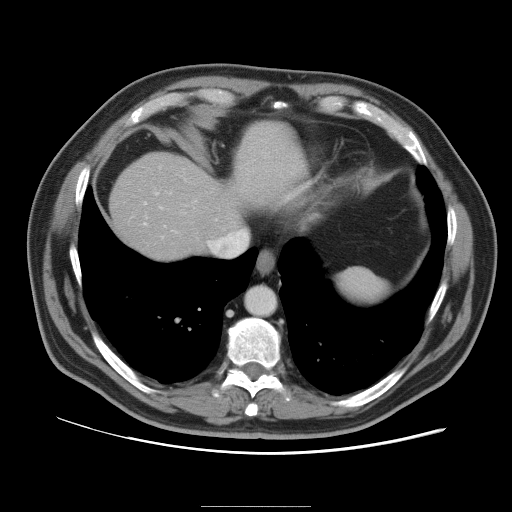
Contrast-enhanced abdominal CT, one axial slice; slice 88 of 105 in the series (ordered by position); 120 kVp; intravenous contrast given; soft-tissue window (W 400 / L 40 HU); 5 mm slice thickness; 512 × 512 image matrix, field of view 399 × 399 mm. Male patient, age 64 years. Case-level facts recorded for this patient, not image findings: diagnosis: colorectal cancer liver metastases, imaged before liver resection; multiple liver metastases: yes; largest metastasis: 3 cm; disease in both lobes: yes.
Annotated regions visible in this slice (outlined manually by an expert reader):
- hepatic veins: bounding box [x1, y1, x2, y2] px = [144, 223, 147, 225]
- liver: [111, 122, 300, 260]
- planned liver remnant (the part of the liver to remain after resection): [111, 157, 227, 259]